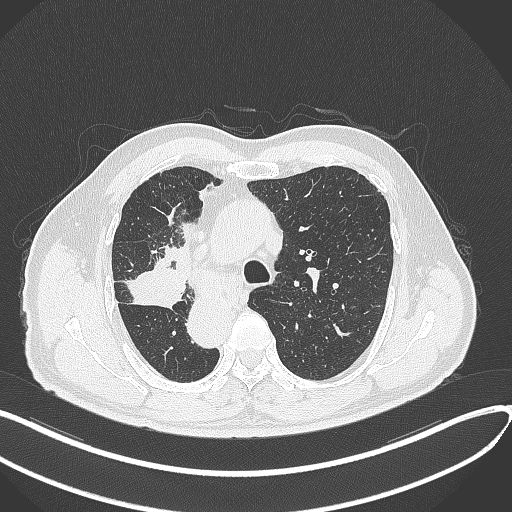
Chest CT, one axial slice. Slice 218 of 300 in the series (ordered by position). Lung window (W 1500 / L -600 HU). 1 mm slice thickness. 512 × 512 image matrix. Male patient, age 67 years. Case-level facts recorded for this patient, not image findings: clinical TNM (as recorded): T2a N0 M0.
Annotated regions visible in this slice (bounding box drawn by a radiologist):
- lung tumour (recorded histology: squamous cell carcinoma): bounding box <123,263,190,313> (left, top, right, bottom; pixels)